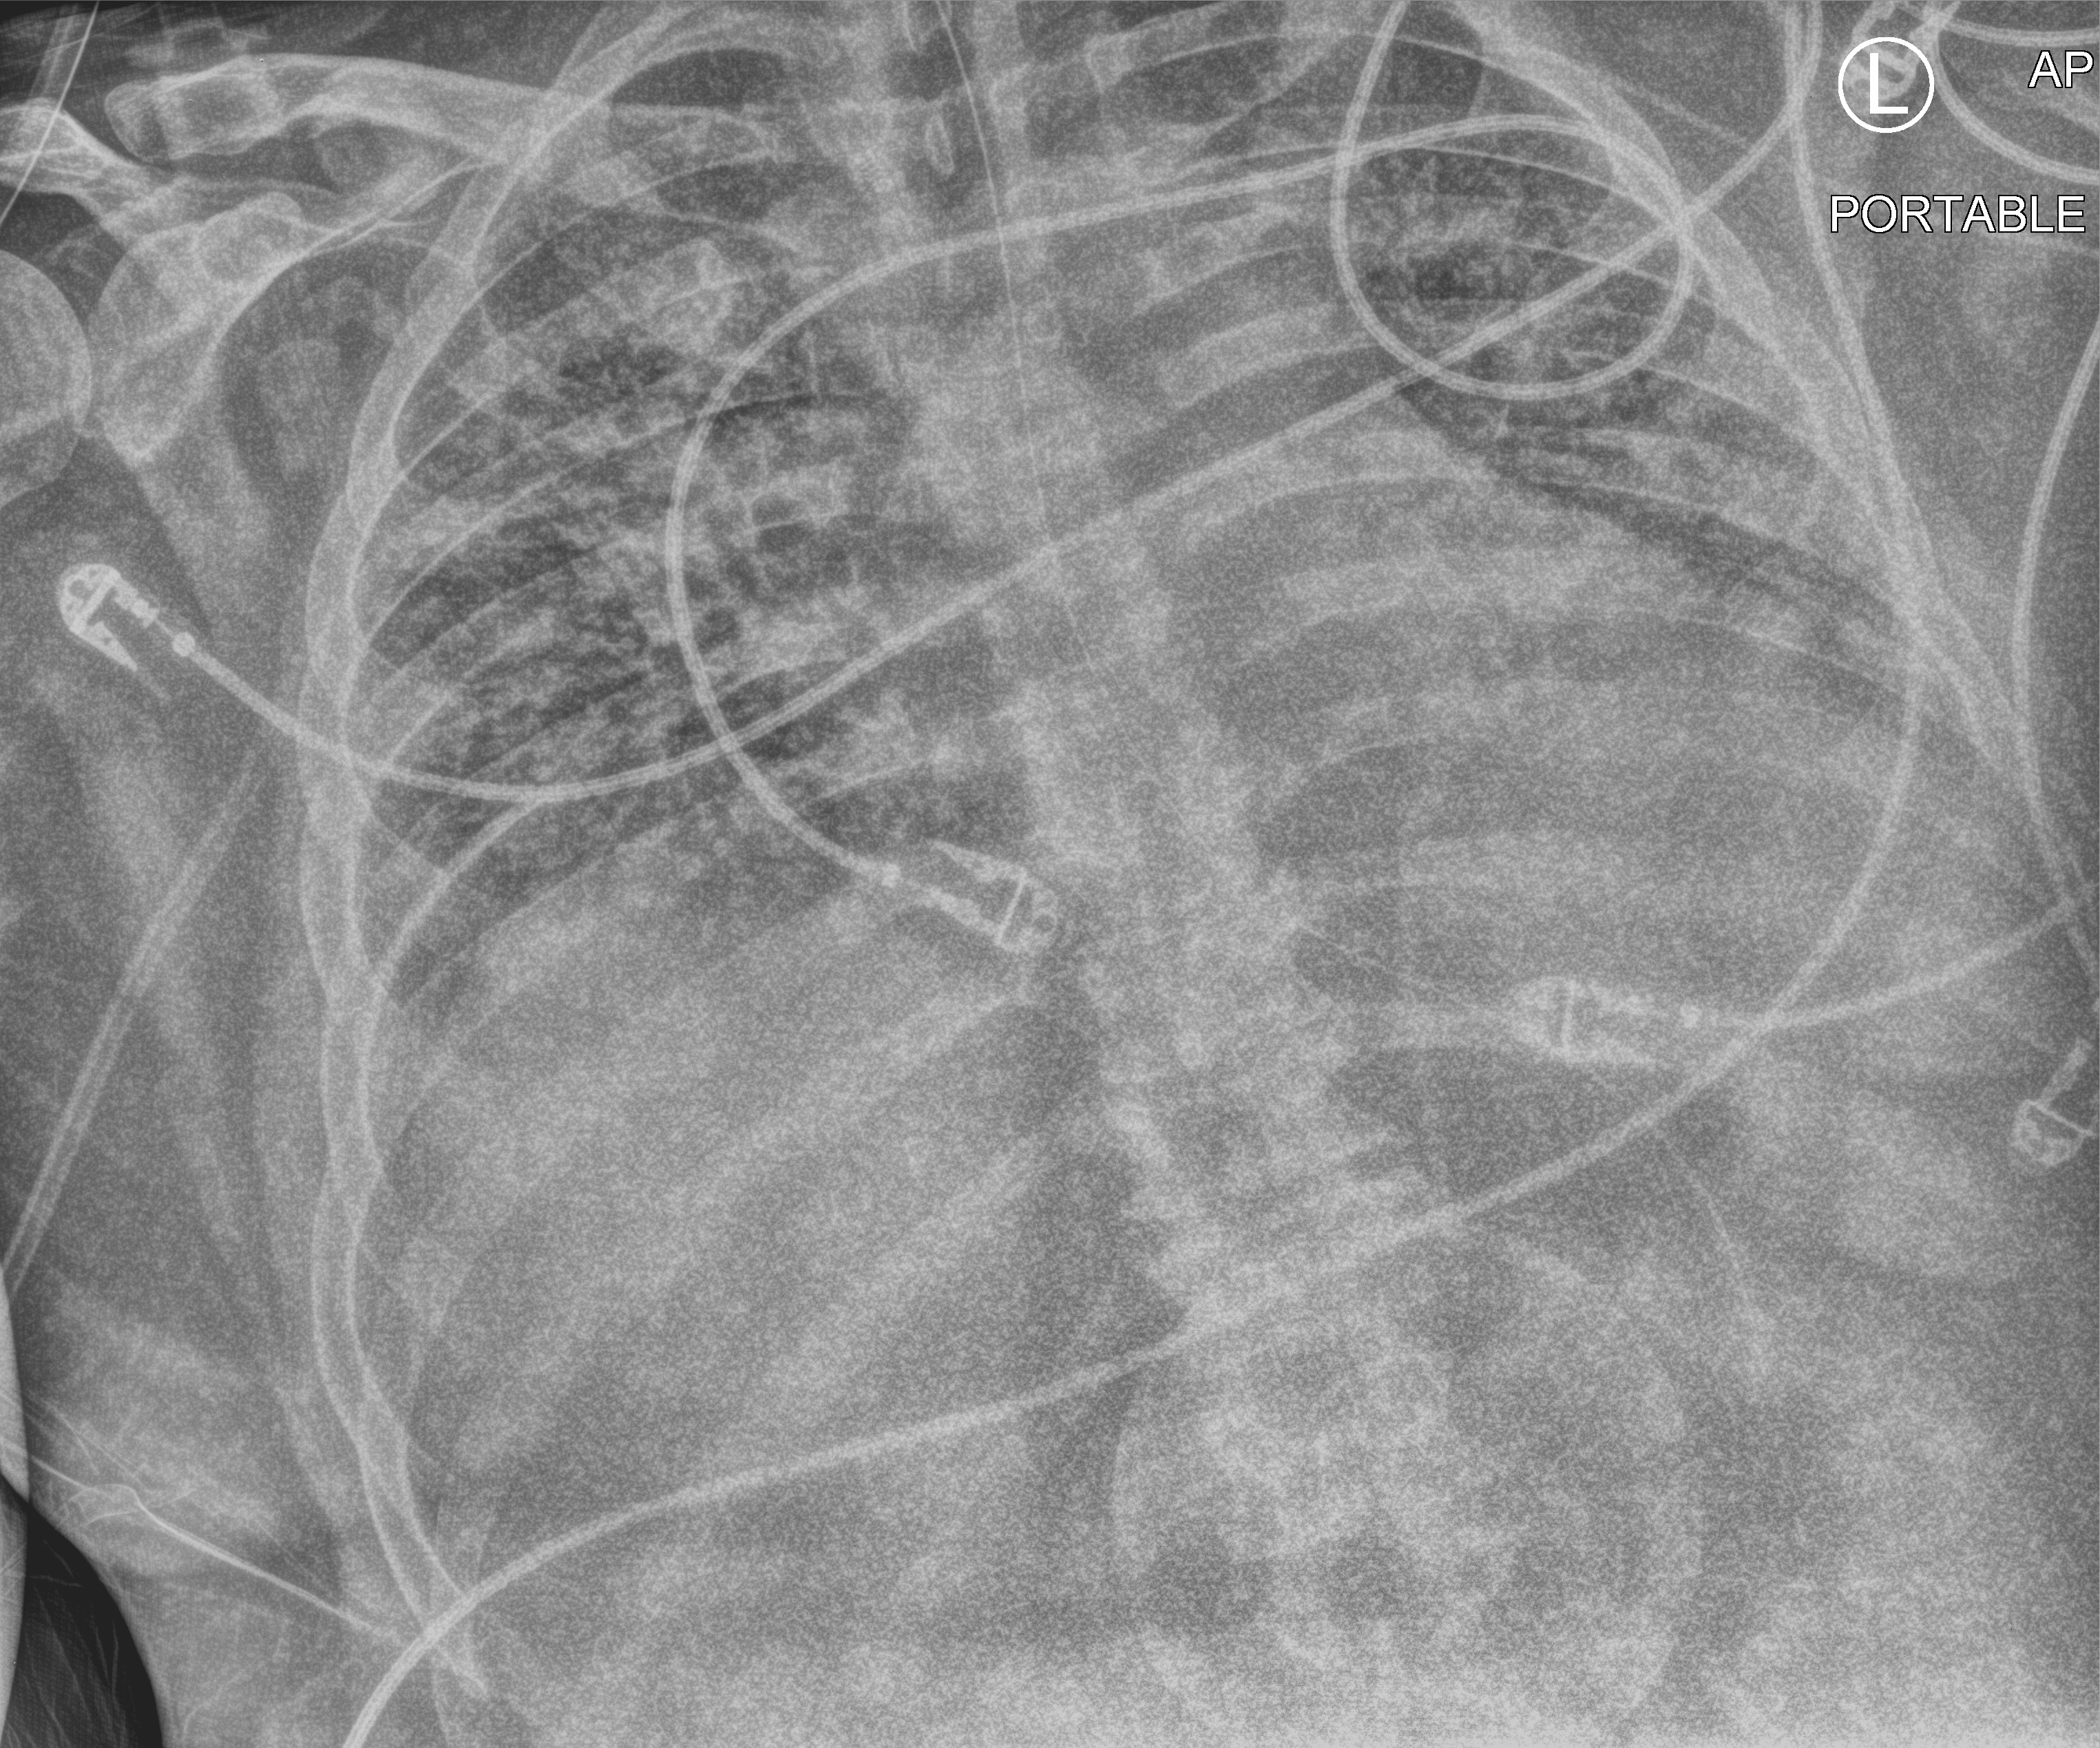
Portable chest radiograph. Patient hospitalised with COVID-19, aged 18–59 years.
From the hospital-stay record, not from the radiograph (when in the stay this image was taken is not recorded):
- mechanically ventilated during this hospital stay: yes
- admitted to intensive care during this hospital stay: yes